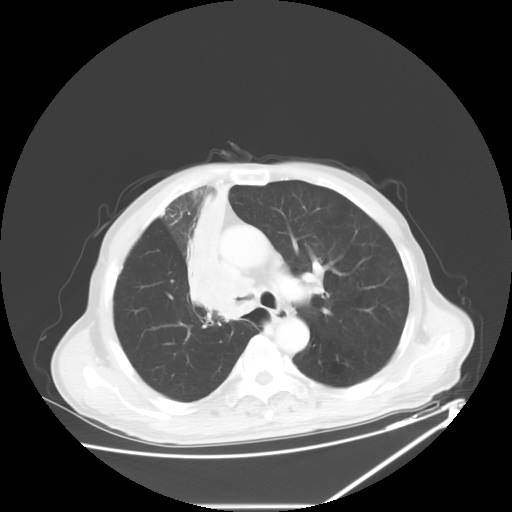
Chest CT, one axial slice; slice 41 of 60 in the series (ordered by position); reconstruction kernel STANDARD; lung window (W 1500 / L -600 HU); 5 mm slice thickness; 512 × 512 image matrix. Male patient, age 73 years. Case-level facts recorded for this patient, not image findings: clinical TNM (as recorded): T2a N1 M0.
Structures marked on this image (rectangle marked by the reading radiologist):
- lung tumour (recorded histology: squamous cell carcinoma): bounding box <182,178,252,331> (left, top, right, bottom; pixels)